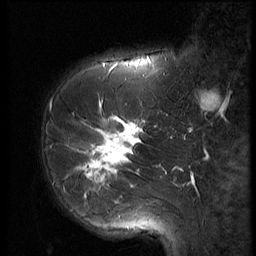
Breast MRI (dynamic contrast-enhanced), one sagittal slice. Position 20 of 56 along the scan axis. 3 images stored at this slice position (order not interpretable as contrast timing). 1.5 T. TE 4.2 ms, TR 9 ms. 2.5 mm slice thickness. 256 × 256 image matrix, field of view 180 × 180 mm. Female patient, age 61 years. From the clinical record (not read from this slice): setting: breast cancer imaged before/during neoadjuvant chemotherapy; receptor status: HR-positive, HER2-negative.
Outlined on this slice (semi-automatically segmented with operator editing):
- analysis volume of interest (the breast-tissue region the enhancement analysis was run in; not a lesion): bounding box (x1, y1, x2, y2) in pixels: (47, 89, 153, 191)
- tumour enhancement mask (voxels above the 140 % enhancement threshold inside the analysis volume of interest): (65, 116, 143, 191)